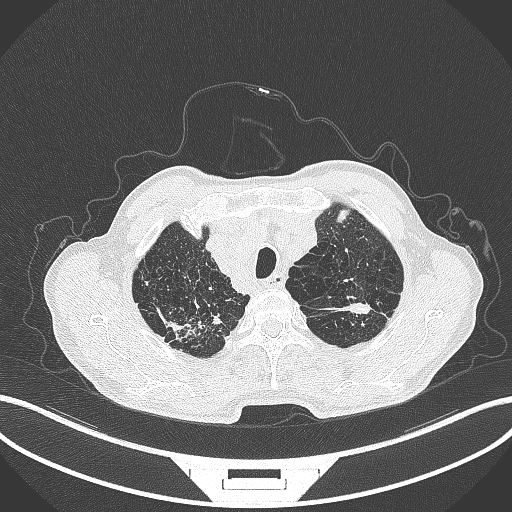
Chest CT, one axial slice; position 383 of 463 along the scan axis; reconstruction kernel B70f; 120 kVp; lung window (W 1500 / L -600 HU); 512 × 512 image matrix, field of view 400 × 400 mm. Patient: male, 74 years. Case-level facts recorded for this patient, not image findings: clinical TNM (as recorded): T2a N1 M0.
Annotated regions visible in this slice (bounding box drawn by a radiologist):
- lung tumour (recorded histology: adenocarcinoma): box from (x=336, y=298) to (x=376, y=316) px